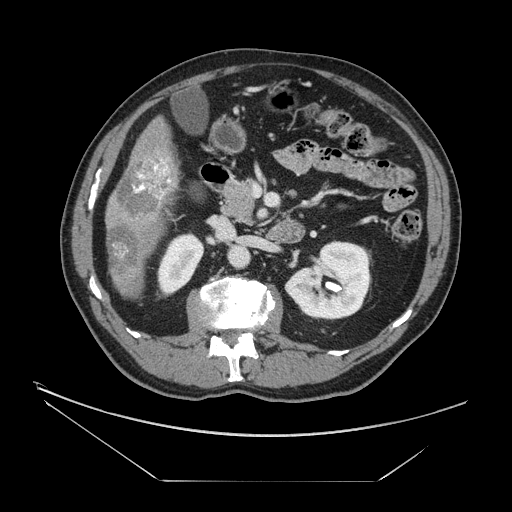
Contrast-enhanced abdominal CT, one axial slice; position 63 of 161 along the scan axis; reconstruction kernel STANDARD; 120 kVp; intravenous contrast given; soft-tissue window (W 400 / L 40 HU); 2.5 mm slice thickness; 512 × 512 image matrix, field of view 440 × 440 mm. Male patient, age 65 years. Case-level facts recorded for this patient, not image findings: diagnosis: colorectal cancer liver metastases, imaged before liver resection; multiple liver metastases: yes; largest metastasis: 4.2 cm; disease in both lobes: yes.
Structures marked on this image (expert manual segmentation):
- liver: box from (x=106, y=119) to (x=180, y=298) px
- portal vein (with intrahepatic branches): (x=134, y=158)–(x=171, y=199)
- liver metastasis: (x=108, y=225)–(x=139, y=276)
- liver metastasis: (x=116, y=159)–(x=174, y=218)